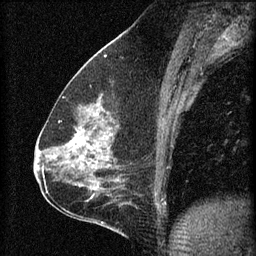
Breast MRI (dynamic contrast-enhanced), one sagittal slice; slice 33 of 60 in the series (ordered by position); 3 images stored at this slice position (order not interpretable as contrast timing); 1.5 T; TE 4.2 ms, TR 8.2 ms; 2 mm slice thickness; 256 × 256 image matrix. Patient: female, 59 years.
Structures marked on this image (semi-automatically segmented with operator editing):
- analysis volume of interest (the breast-tissue region the enhancement analysis was run in; not a lesion): box from (x=61, y=104) to (x=122, y=161) px
- tumour enhancement mask (voxels above the 70 % enhancement threshold inside the analysis volume of interest): (x=70, y=132)–(x=109, y=159)